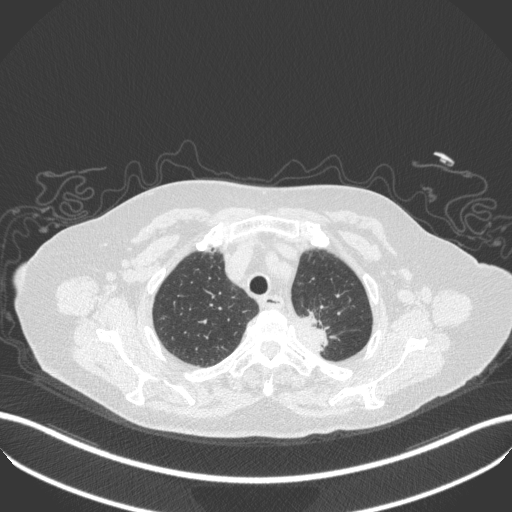
Chest CT, one axial slice. Slice 284 of 353 in the series (ordered by position). Lung window (W 1500 / L -600 HU). 512 × 512 image matrix, field of view 400 × 400 mm. Female patient, age 81 years. Case-level facts recorded for this patient, not image findings: clinical TNM (as recorded): T2a N0 M0.
Annotated regions visible in this slice (bounding box drawn by a radiologist):
- lung tumour (recorded histology: adenocarcinoma): bounding box <287,306,337,353> (left, top, right, bottom; pixels)